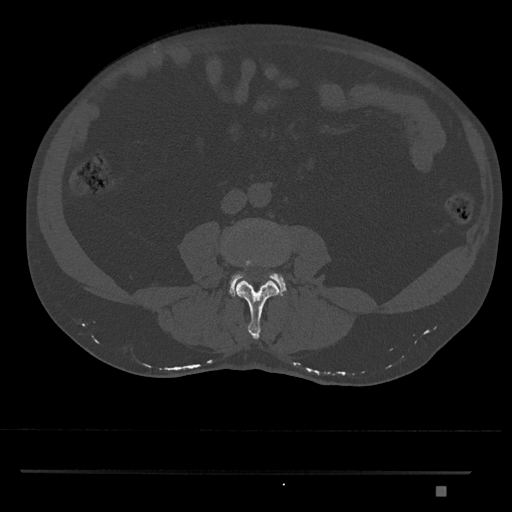
CT including the spine, one axial slice; position 657 of 1134 along the scan axis; bone window (W 1800 / L 400 HU); 0.5 mm slice thickness; 512 × 512 image matrix, field of view 429 × 429 mm. Male patient, age 65 years. From the clinical record (not read from this slice): primary cancer: prostate.
Structures marked on this image (semi-automatically segmented with operator editing):
- L3 vertebra: bounding box (x1, y1, x2, y2) in pixels: (222, 222, 280, 340)
- L4 vertebra: (229, 272, 287, 297)